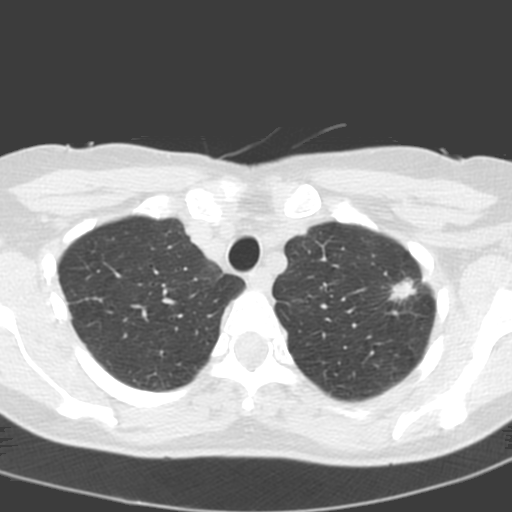
Low-dose screening chest CT, axial slice, baseline annual screen, lung window (W 1500 / L -600 HU), 3.2 mm slice thickness, standard (soft-tissue) reconstruction kernel (C), slice 34 of 193 in the series, 512 × 512 image matrix. Female participant, aged 58 years at enrolment.
Lesion marked by an expert reader, bounding box [x1, y1, x2, y2] px = [379, 269, 427, 317]. The exam's reader record, not a measurement of the box and not confirmed to be the same lesion: non-calcified nodule or mass ≥4 mm, left upper lobe, 14 × 10 mm, spiculated (stellate) margins, soft tissue attenuation. Lung cancer was diagnosed 48 days after this screen: adenocarcinoma, NOS, left upper lobe, poorly differentiated (G3), stage IA (AJCC 6th edition), 13 mm at pathology.